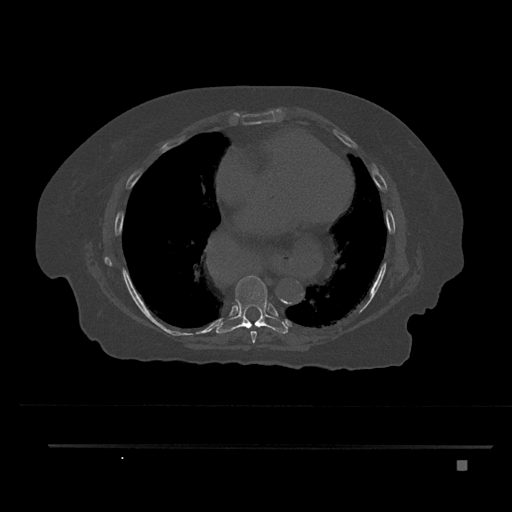
CT including the spine, one axial slice; position 453 of 797 along the scan axis; reconstruction kernel Br40s/3; 120 kVp; bone window (W 1800 / L 400 HU); 512 × 512 image matrix. Female patient, age 76 years. From the clinical record (not read from this slice): primary cancer: lung; vertebrae with lytic lesions (as recorded): T11, L3.
Structures marked on this image (semi-automatic segmentation, software-assisted and operator-edited):
- T7 vertebra: bounding box (x1, y1, x2, y2) in pixels: (250, 331, 257, 343)
- T8 vertebra: (216, 275, 289, 334)